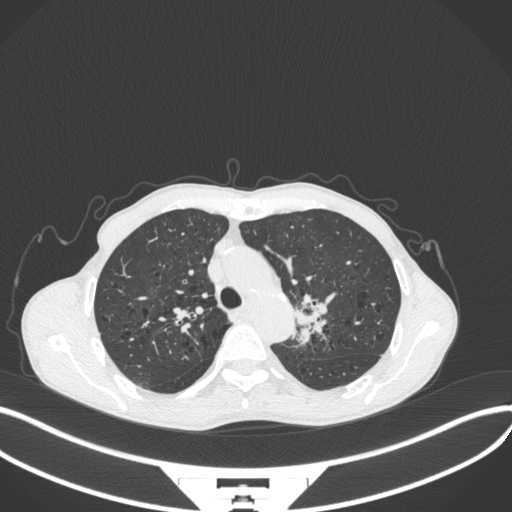
Chest CT, one axial slice; position 306 of 394 along the scan axis; reconstruction kernel B31f; lung window (W 1500 / L -600 HU); 1 mm slice thickness; 512 × 512 image matrix. Male patient, age 65 years. From the clinical record (not read from this slice): clinical TNM (as recorded): T2b N0 M0; histopathological grade: G2.
Structures marked on this image (rectangle marked by the reading radiologist):
- lung tumour (recorded histology: adenocarcinoma): box from (x=290, y=292) to (x=332, y=349) px